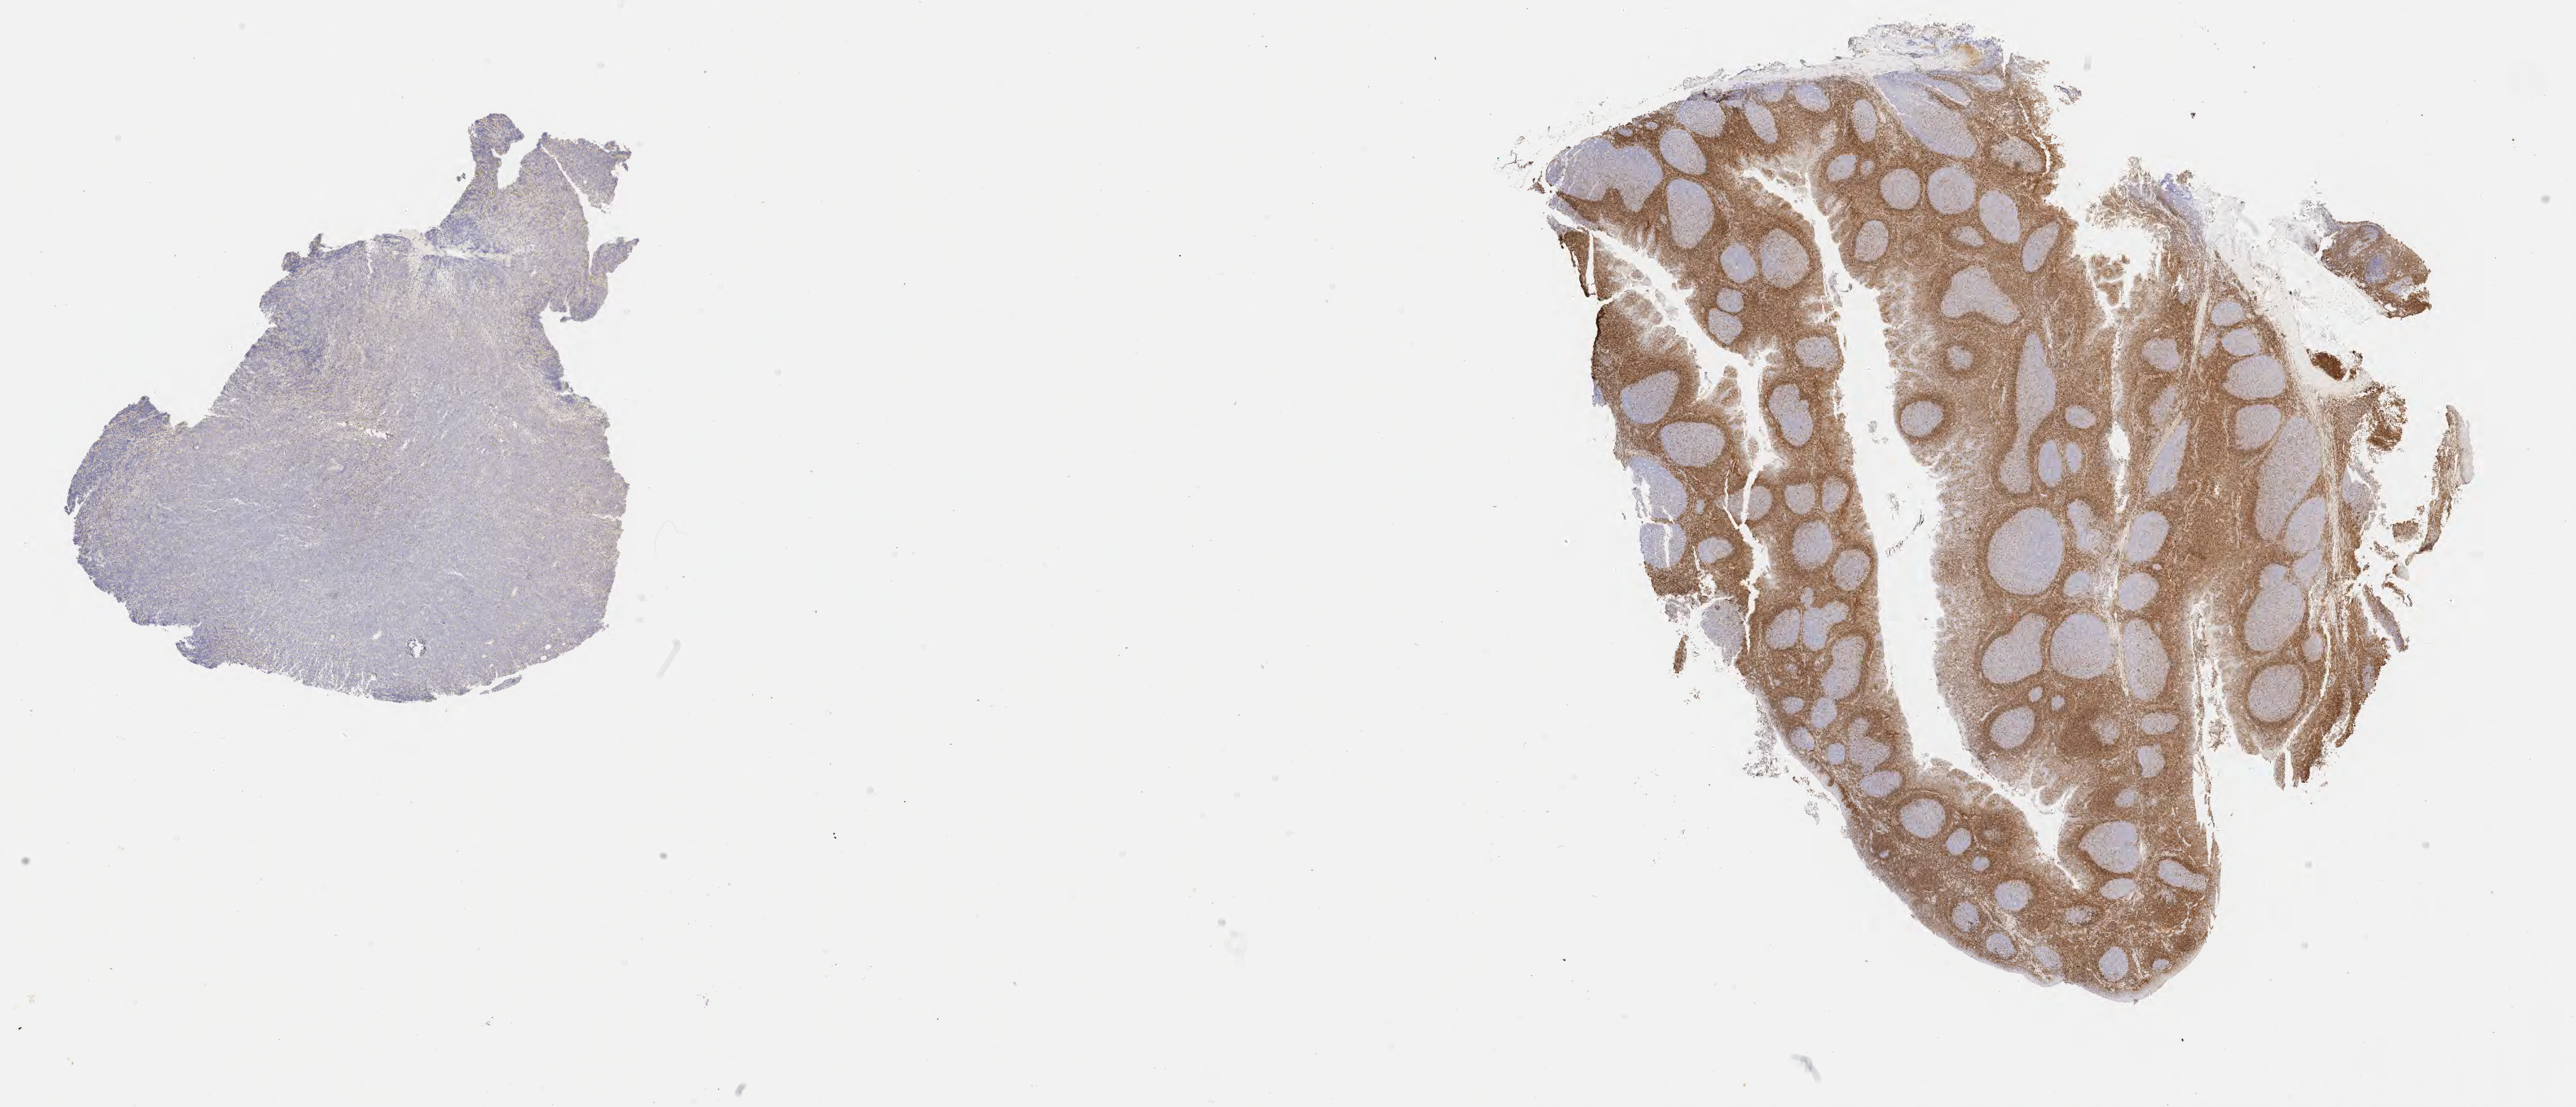
Whole-slide image, immunohistochemical stain for BCL2 — low-resolution overview of the scanned area, about 32.2 x 13.8 mm, tumor tissue, anatomic site: mandible. Female, age 5 years at initial diagnosis.
- histologic diagnosis: Burkitt lymphoma, NOS